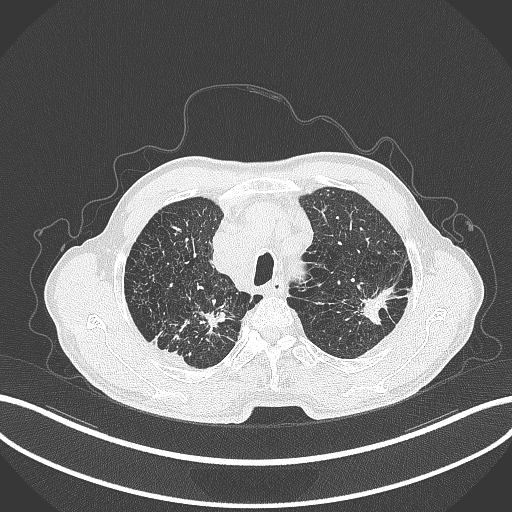
Chest CT, one axial slice. Slice 366 of 463 in the series (ordered by position). Lung window (W 1500 / L -600 HU). 1 mm slice thickness. 512 × 512 image matrix. Male patient, age 74 years. Case-level facts recorded for this patient, not image findings: clinical TNM (as recorded): T2a N1 M0.
Annotated regions visible in this slice (rectangle marked by the reading radiologist):
- lung tumour (recorded histology: adenocarcinoma): bounding box (x1, y1, x2, y2) in pixels: (355, 272, 400, 327)